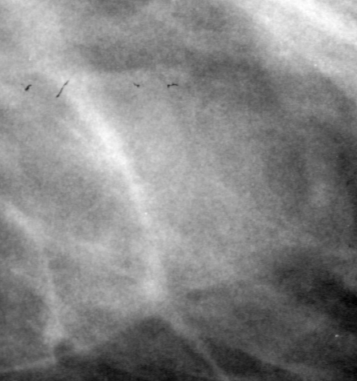
Crop from a digitized film mammogram around one marked abnormality; right breast; MLO view; BI-RADS breast density category 1 (scale 1–4).
Finding: mass, shape oval, margins obscured; BI-RADS assessment category 3; subtlety rating 3 on a 1 (subtle) to 5 (obvious) scale; pathology result (as recorded, not read from the image): benign.